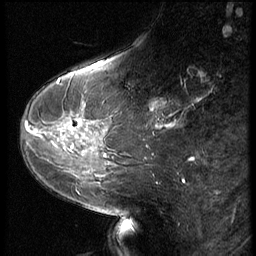
Breast MRI (dynamic contrast-enhanced), one sagittal slice. Slice 23 of 66 in the series (ordered by position). 3 images stored at this slice position (order not interpretable as contrast timing). 1.5 T. TE 4.2 ms, TR 9 ms. 2.5 mm slice thickness. 256 × 256 image matrix, field of view 180 × 180 mm. Patient: female, 54 years. Case-level facts recorded for this patient, not image findings: setting: breast cancer imaged before/during neoadjuvant chemotherapy; receptor status: HR-positive, HER2-negative.
Annotated regions visible in this slice (semi-automatic segmentation, software-assisted and operator-edited):
- analysis volume of interest (the breast-tissue region the enhancement analysis was run in; not a lesion): box from (x=24, y=110) to (x=94, y=159) px
- tumour enhancement mask (voxels above the 140 % enhancement threshold inside the analysis volume of interest): (x=27, y=123)–(x=82, y=127)